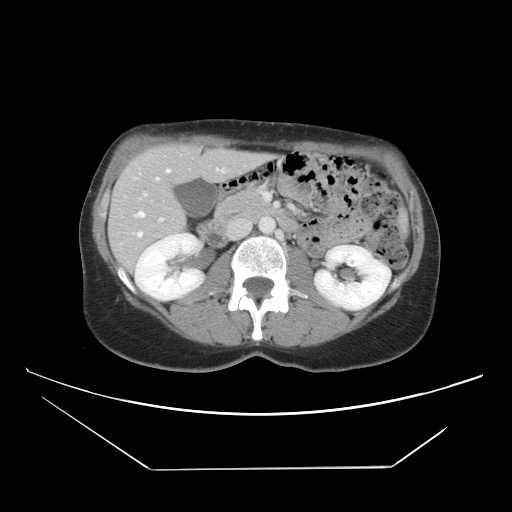
Contrast-enhanced abdominal CT, one axial slice. Position 20 of 42 along the scan axis. 120 kVp. Intravenous contrast given. Soft-tissue window (W 400 / L 40 HU). 512 × 512 image matrix. Female patient, age 52 years. Case-level facts recorded for this patient, not image findings: diagnosis: colorectal cancer liver metastases, imaged before liver resection; multiple liver metastases: yes; largest metastasis: 5.5 cm; disease in both lobes: yes.
Structures marked on this image (outlined manually by an expert reader):
- hepatic veins: bounding box (x1, y1, x2, y2) in pixels: (132, 165, 225, 238)
- liver: (110, 143, 264, 268)
- planned liver remnant (the part of the liver to remain after resection): (115, 143, 215, 209)
- portal vein (with intrahepatic branches): (143, 165, 270, 222)